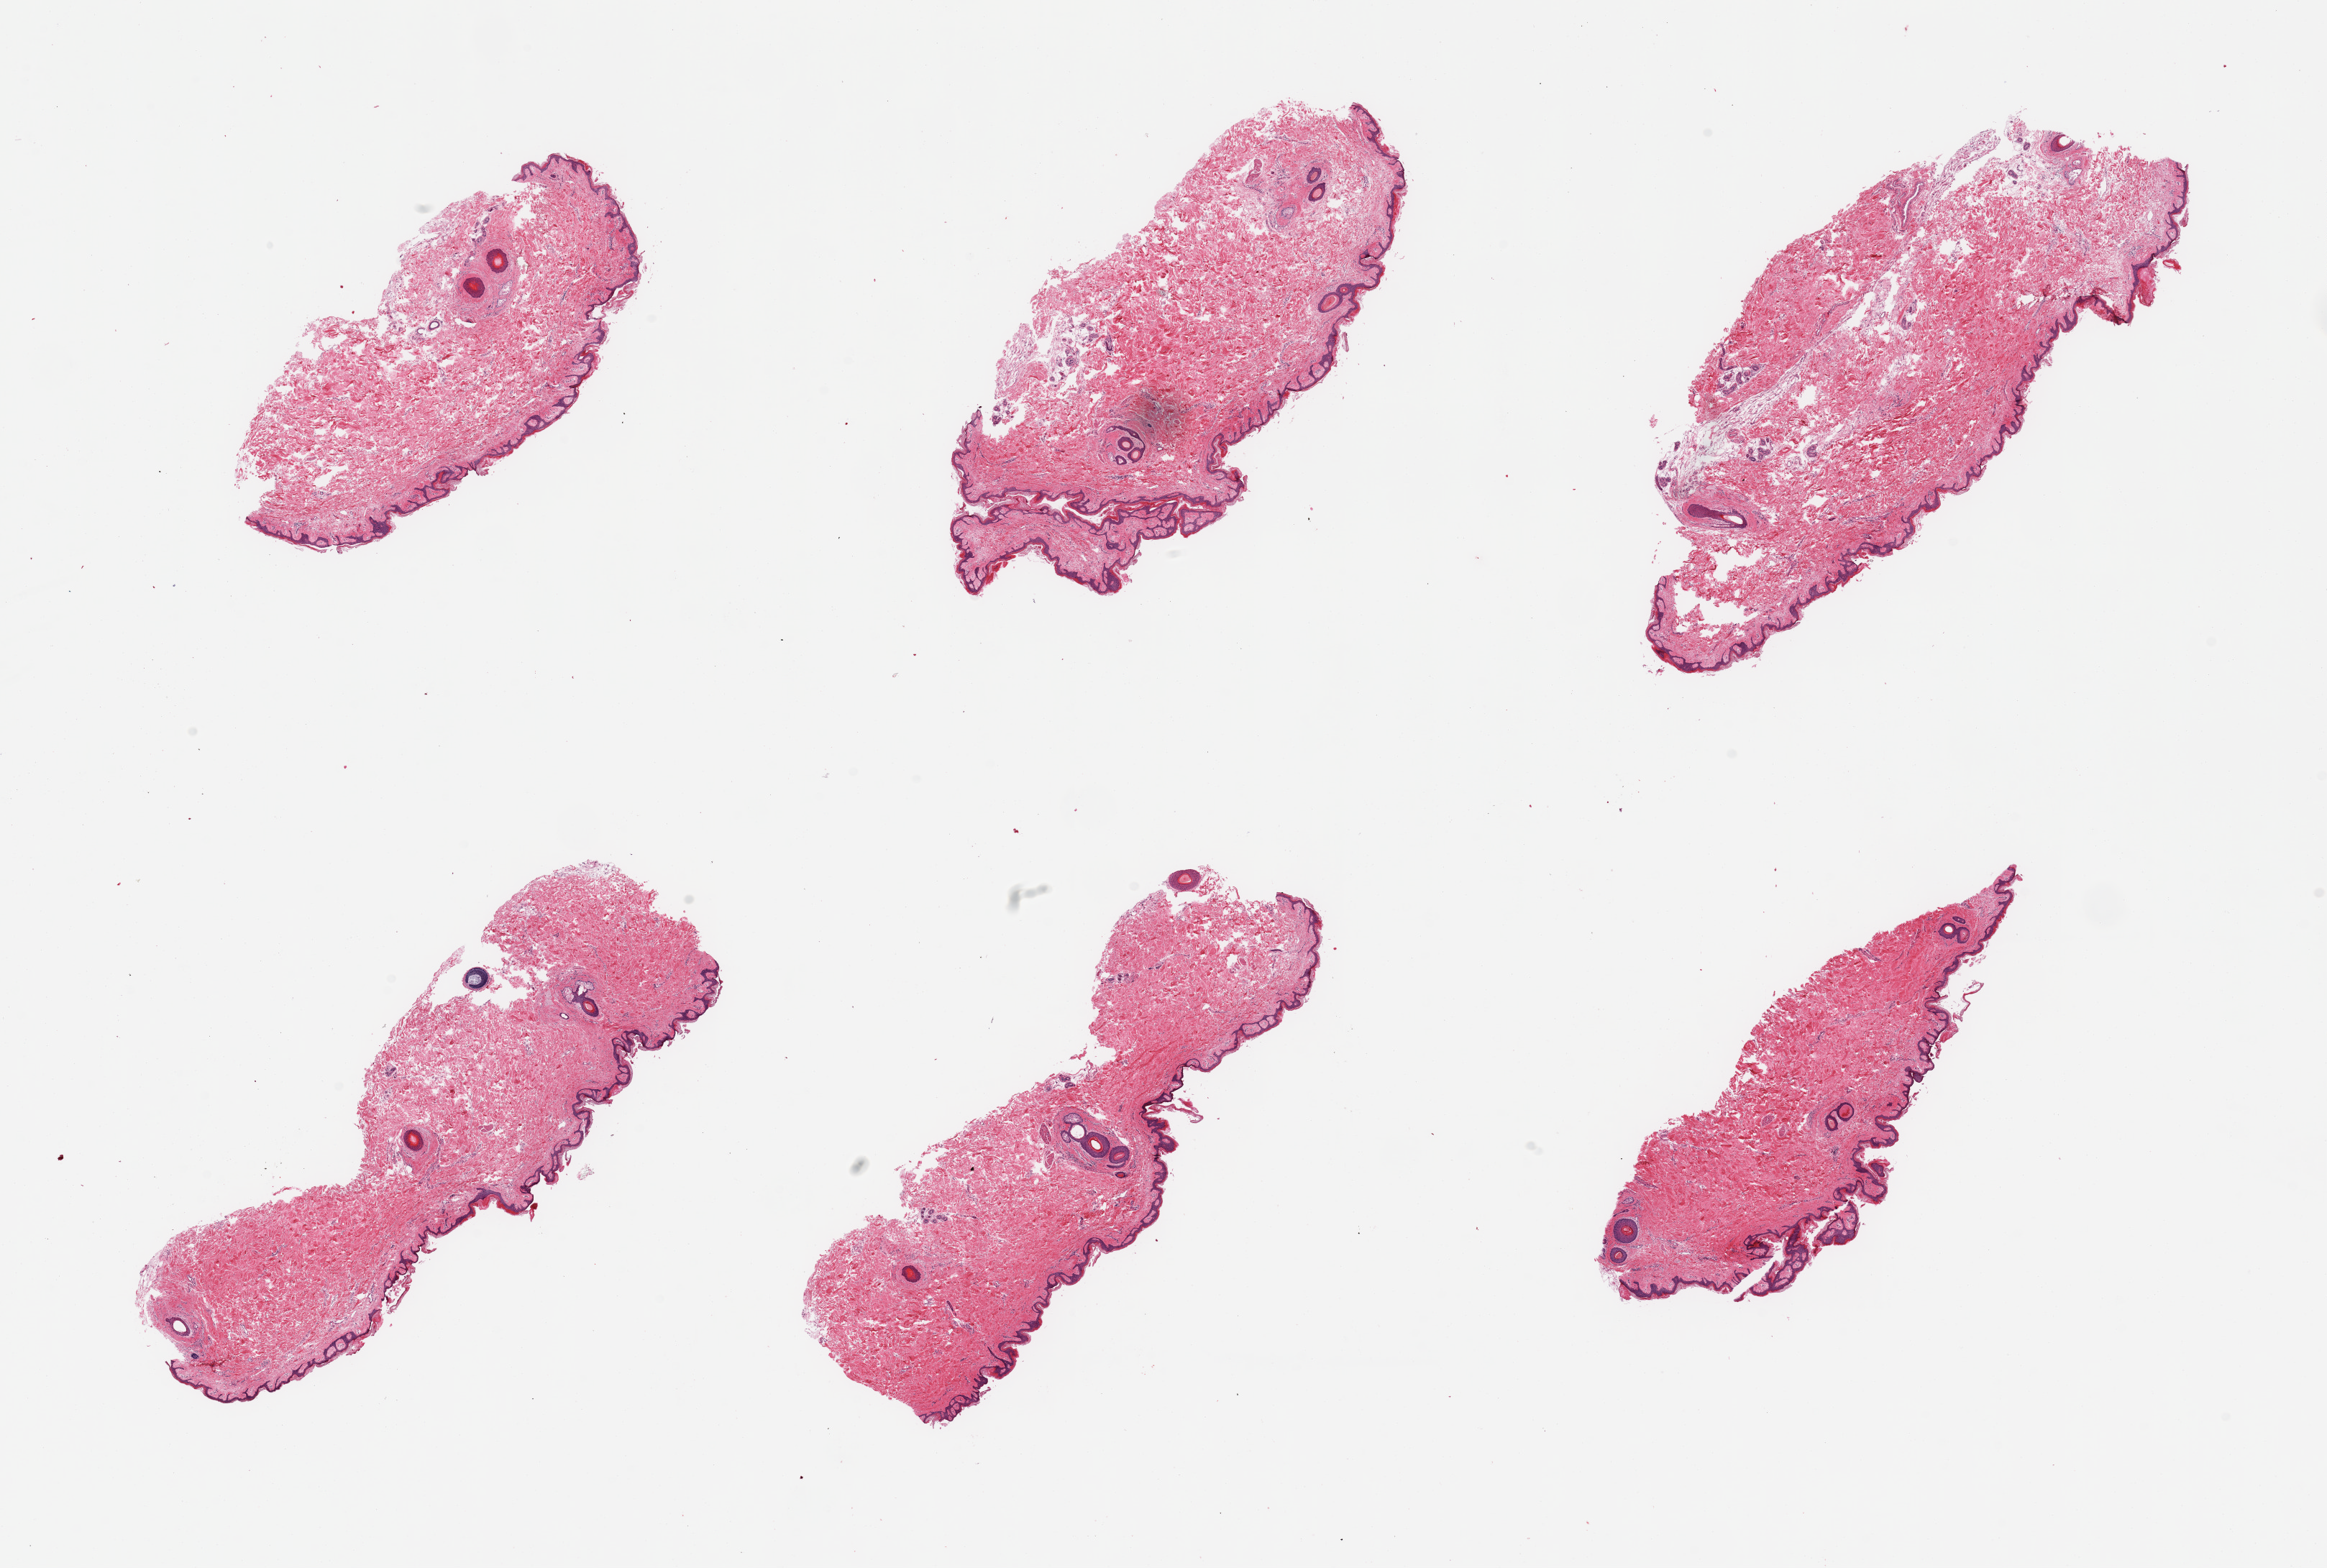
Digitized H&E-stained section, brightfield — shown as a low-resolution overview of the whole scanned area (about 25.6 x 17.3 mm, from a 20x scan); PAXgene-fixed paraffin-embedded (PFPE) section; section of skin of suprapubic region (target tissue); donor tissue sample. Donor sex: male.
Reviewer comment on this tissue sample: 6 pieces, minimal dermal fat; squamous epithelium is ~30 microns.